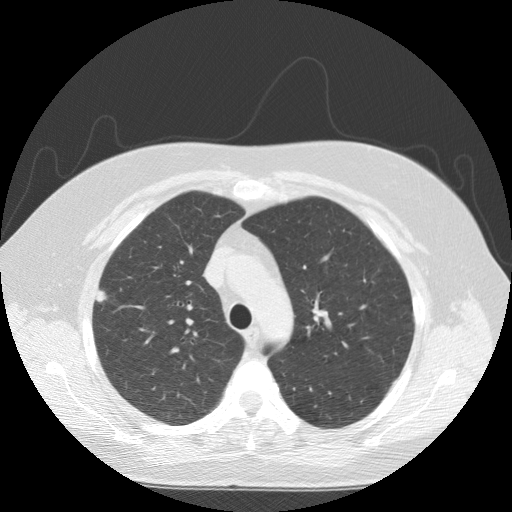
Axial slice from a low-dose chest CT screening exam; baseline screening round; lung window (W 1500 / L -600 HU); 2.5 mm slice thickness; standard (soft-tissue) reconstruction kernel (STANDARD). Female participant, aged 55 years at enrolment. Current smoker at enrolment.
Lesion marked by an expert reader, bounding box (x1, y1, x2, y2) in pixels: (82, 282, 120, 319). Screening reader's record for this exam (one nodule recorded; not confirmed to be the boxed lesion): non-calcified nodule or mass ≥4 mm, right upper lobe, 8 × 7 mm, spiculated (stellate) margins, soft tissue attenuation. Official screen result: positive, change unspecified: nodule(s) >= 4 mm or enlarging nodule(s), mass(es), or other non-specific abnormalities suspicious for lung cancer. Lung cancer was diagnosed 98 days after this screen: squamous cell carcinoma, NOS, right upper lobe, poorly differentiated (G3), stage IA (AJCC 6th edition), 8 mm at pathology.